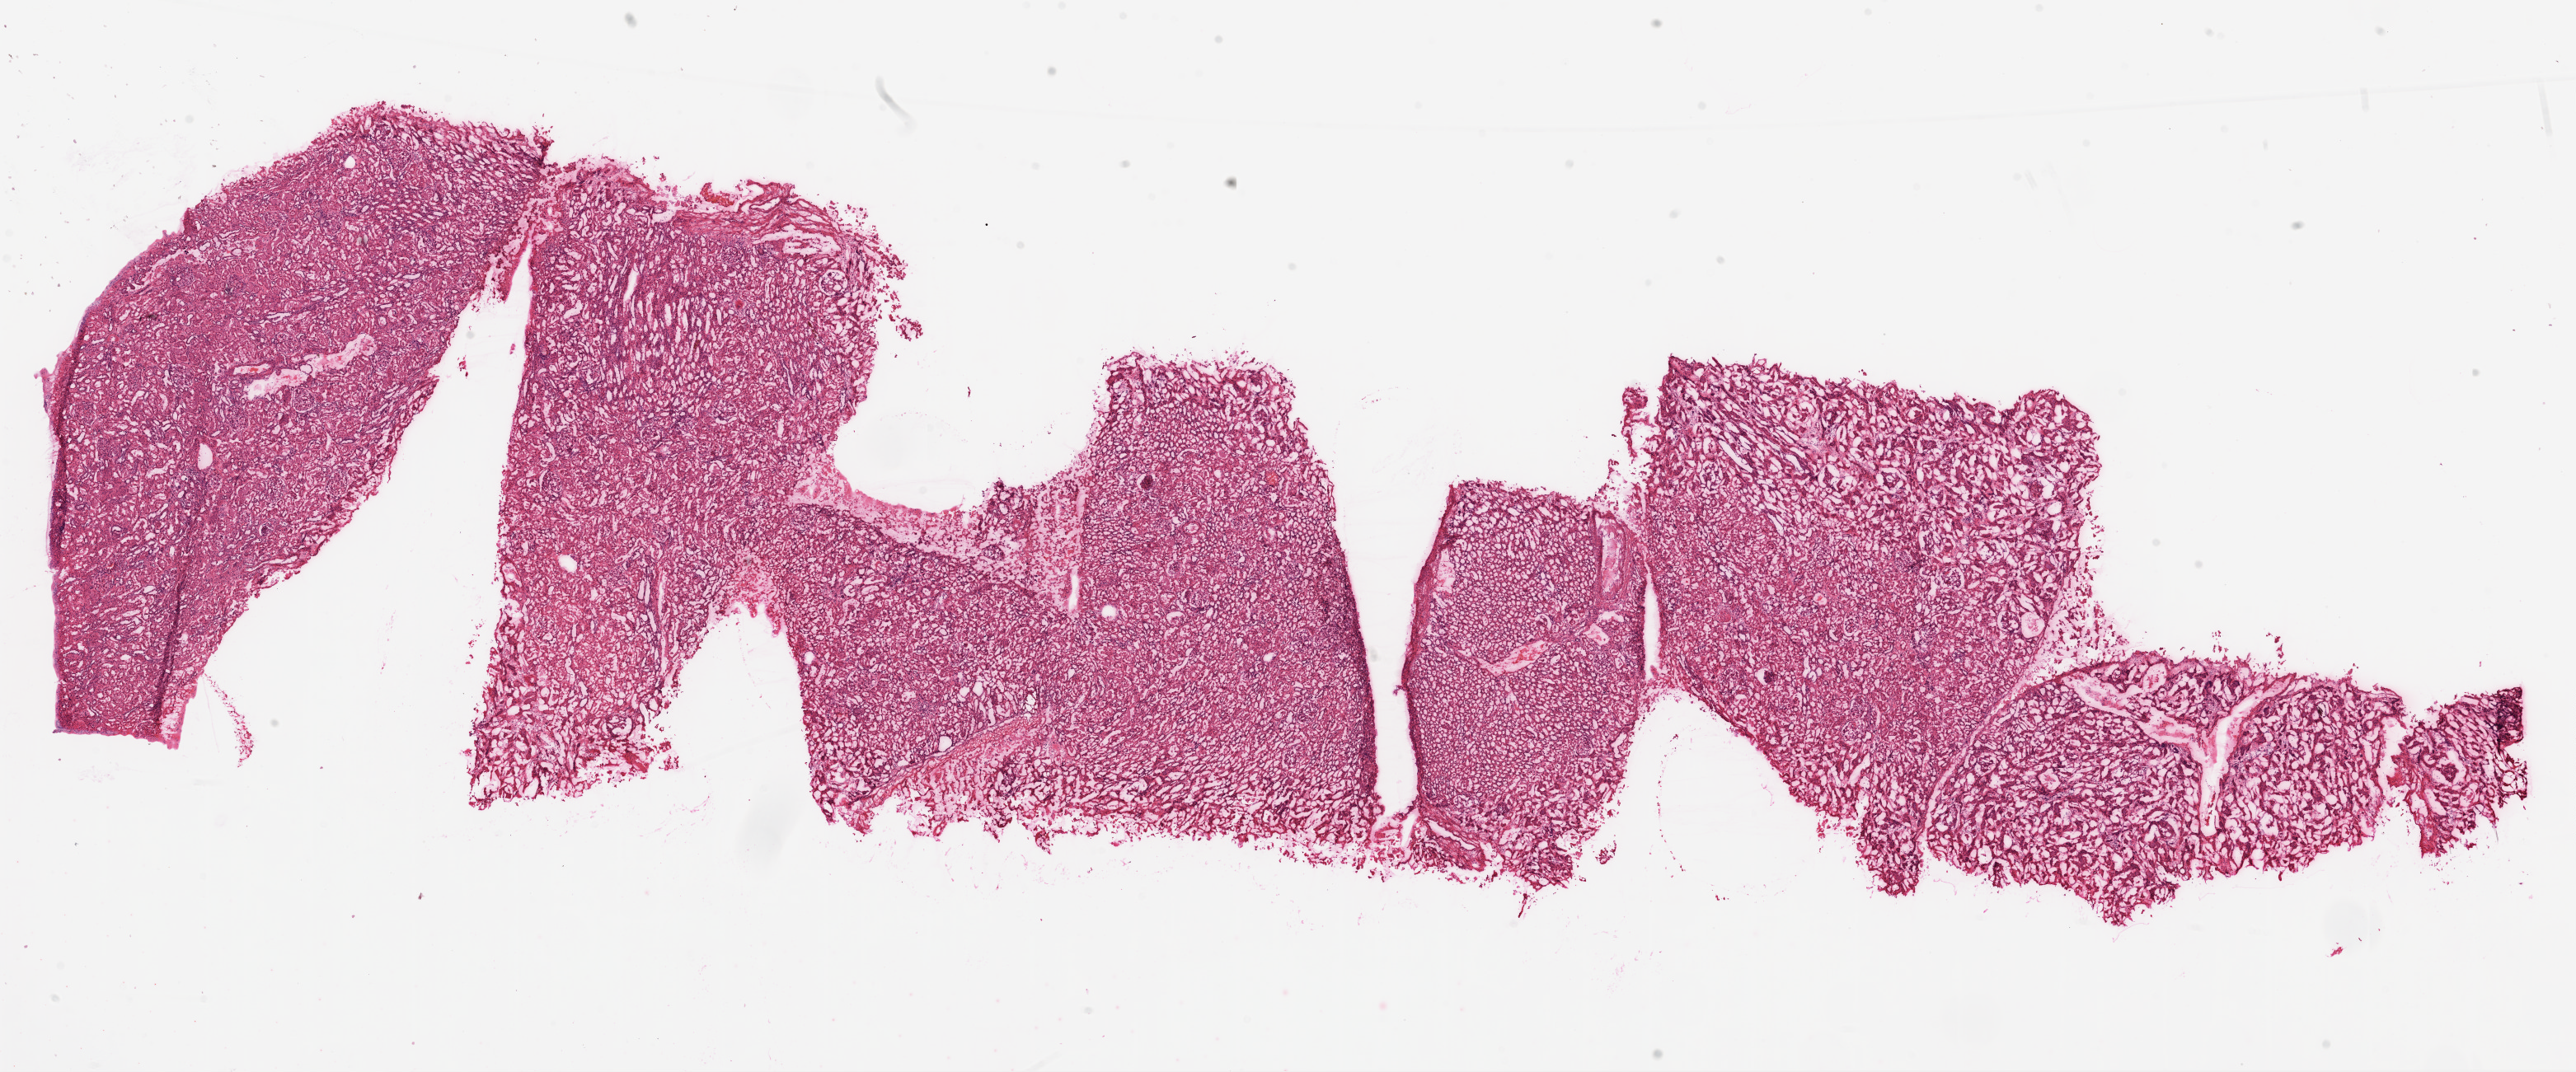
Digitized H&E tissue section (whole slide) — whole scanned area (about 25.1 x 10.4 mm) shown as a low-resolution overview, frozen section, sample: solid tissue normal (non-tumour tissue), kidney. Male patient; age at initial diagnosis 62 years.
This section: solid tissue normal sample (biorepository sample class). Patient diagnosis: Clear cell adenocarcinoma, NOS.